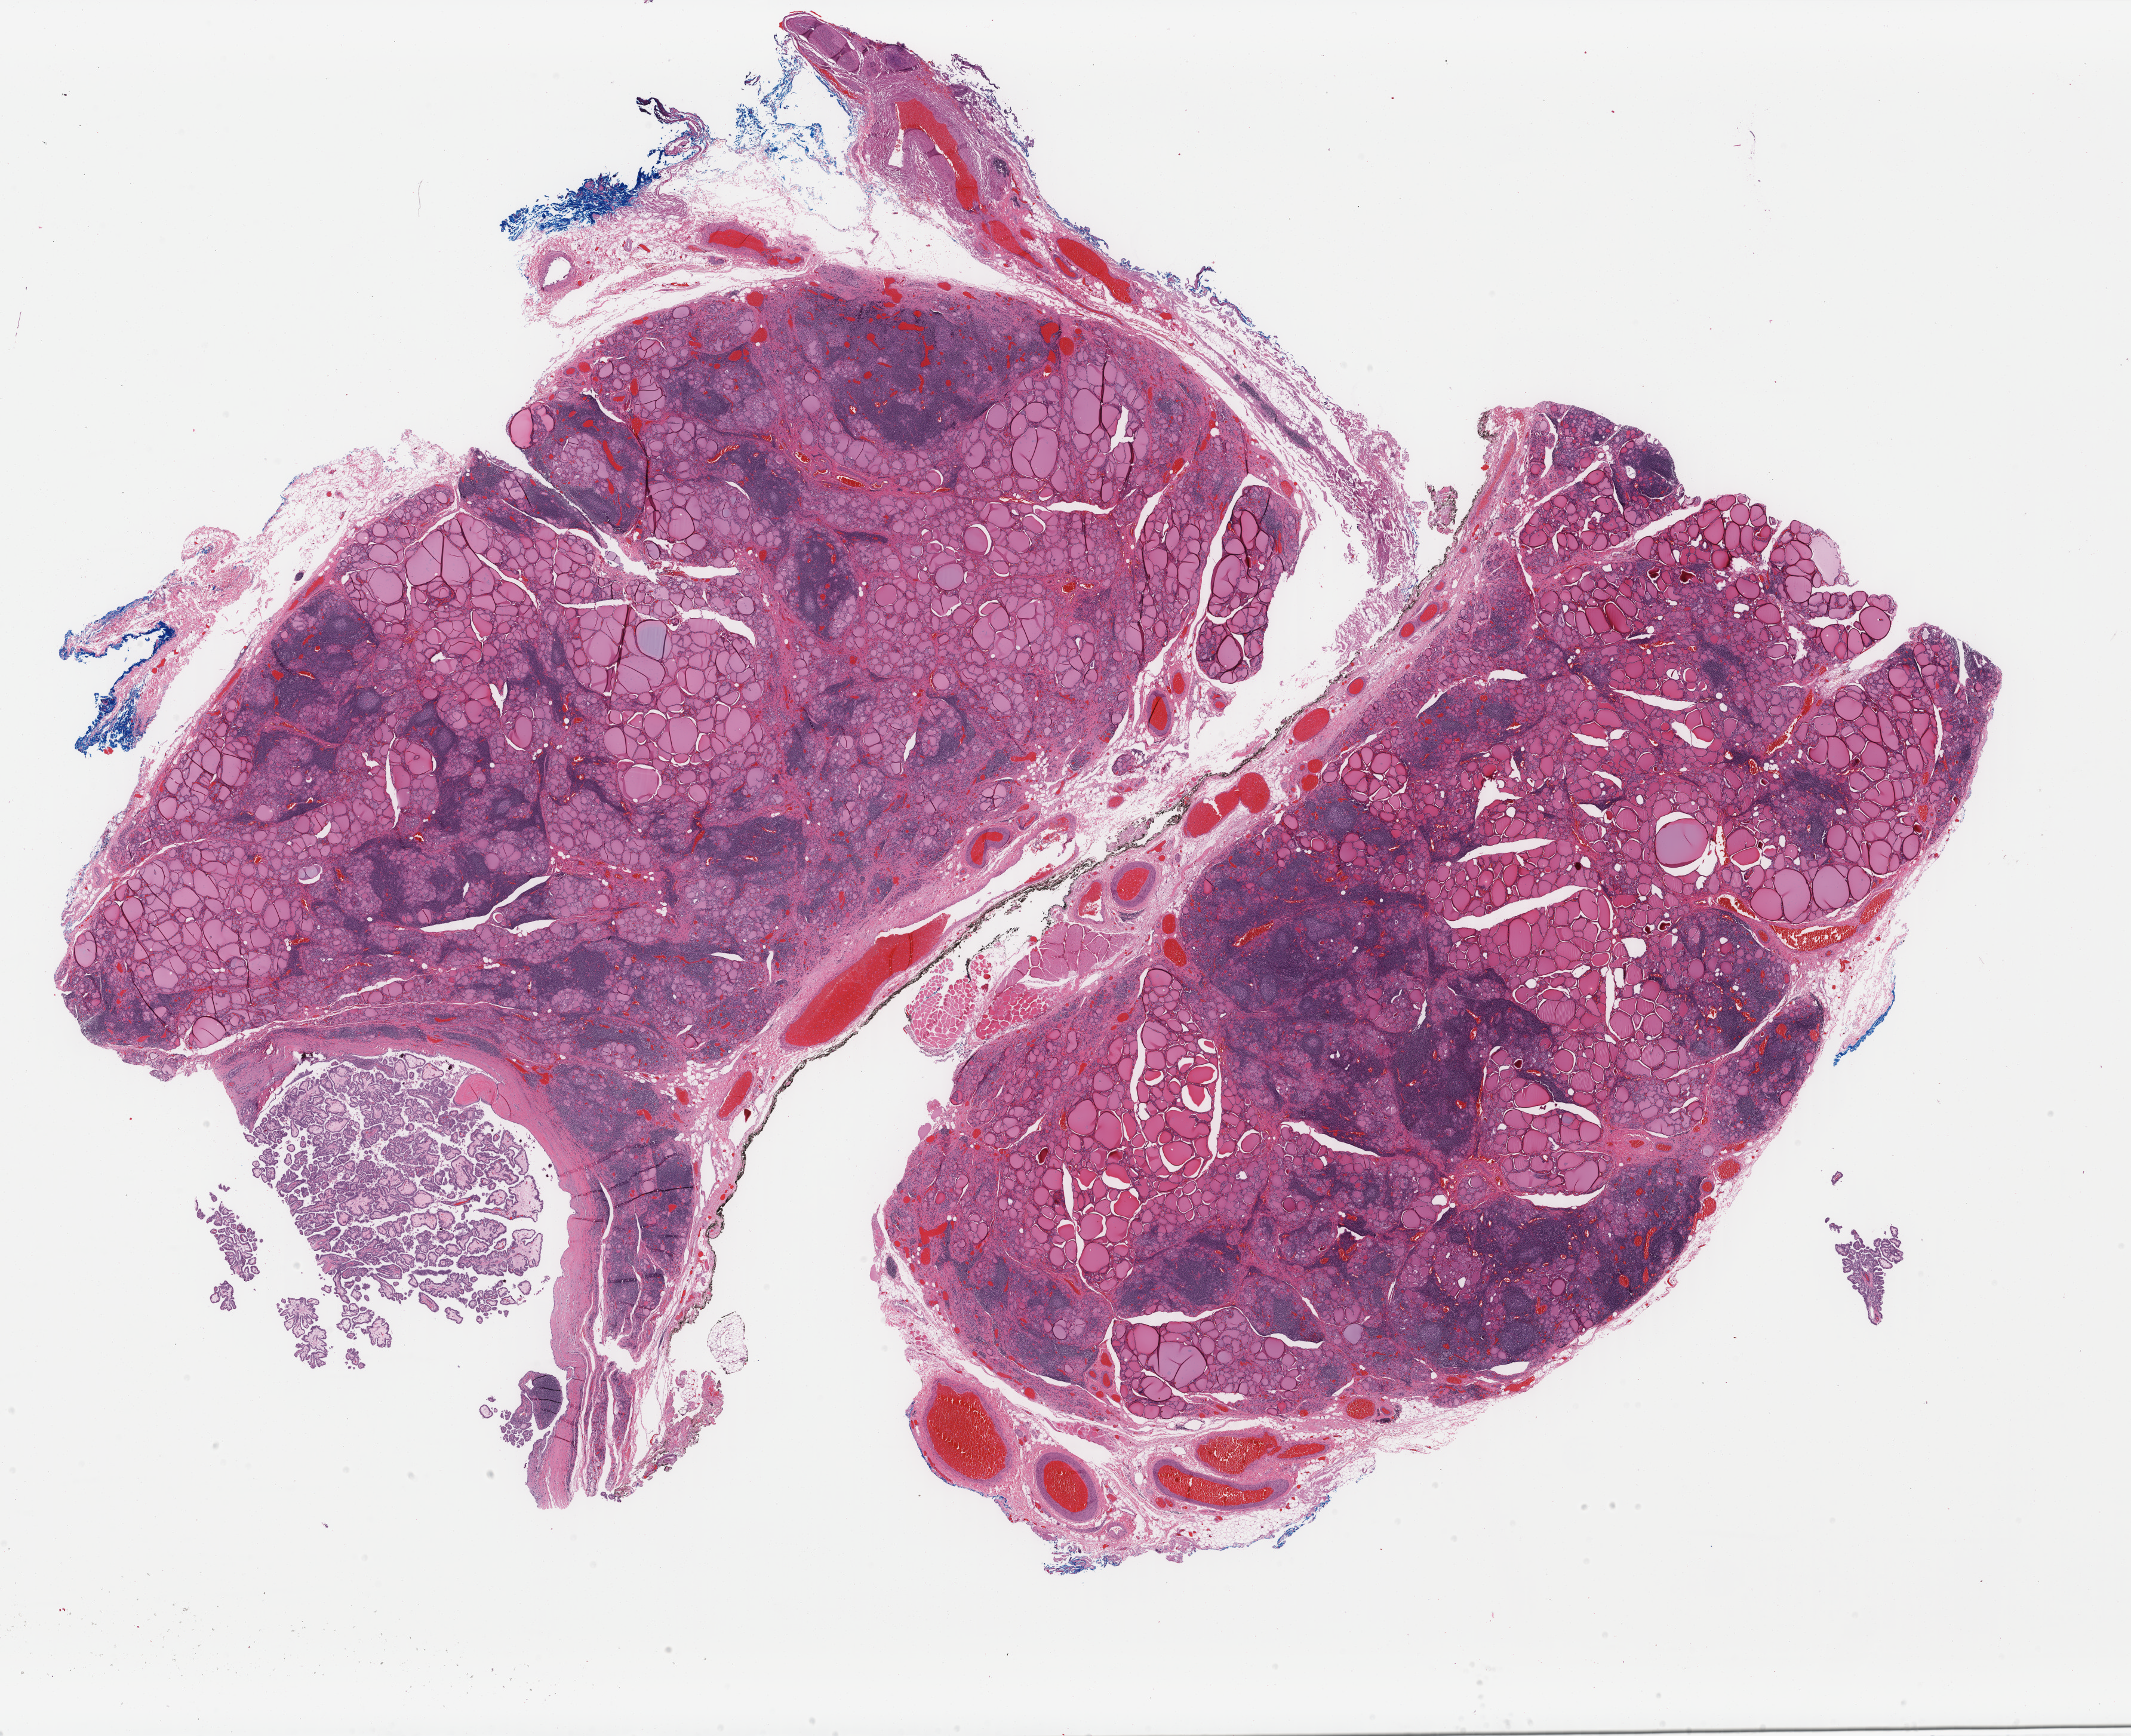
Hematoxylin and eosin (H&E) stained whole-slide image, a low-resolution overview of the entire scanned area, about 28.3 x 23.1 mm, formalin-fixed paraffin-embedded (FFPE) diagnostic section, sample: primary tumour, thyroid. Patient: male, age at initial diagnosis 53 years.
Pathologic diagnosis: Papillary adenocarcinoma, NOS (thyroid gland). Lymph nodes positive (case pathology): 1 of 10 examined. AJCC pathologic stage: III (7th edition).